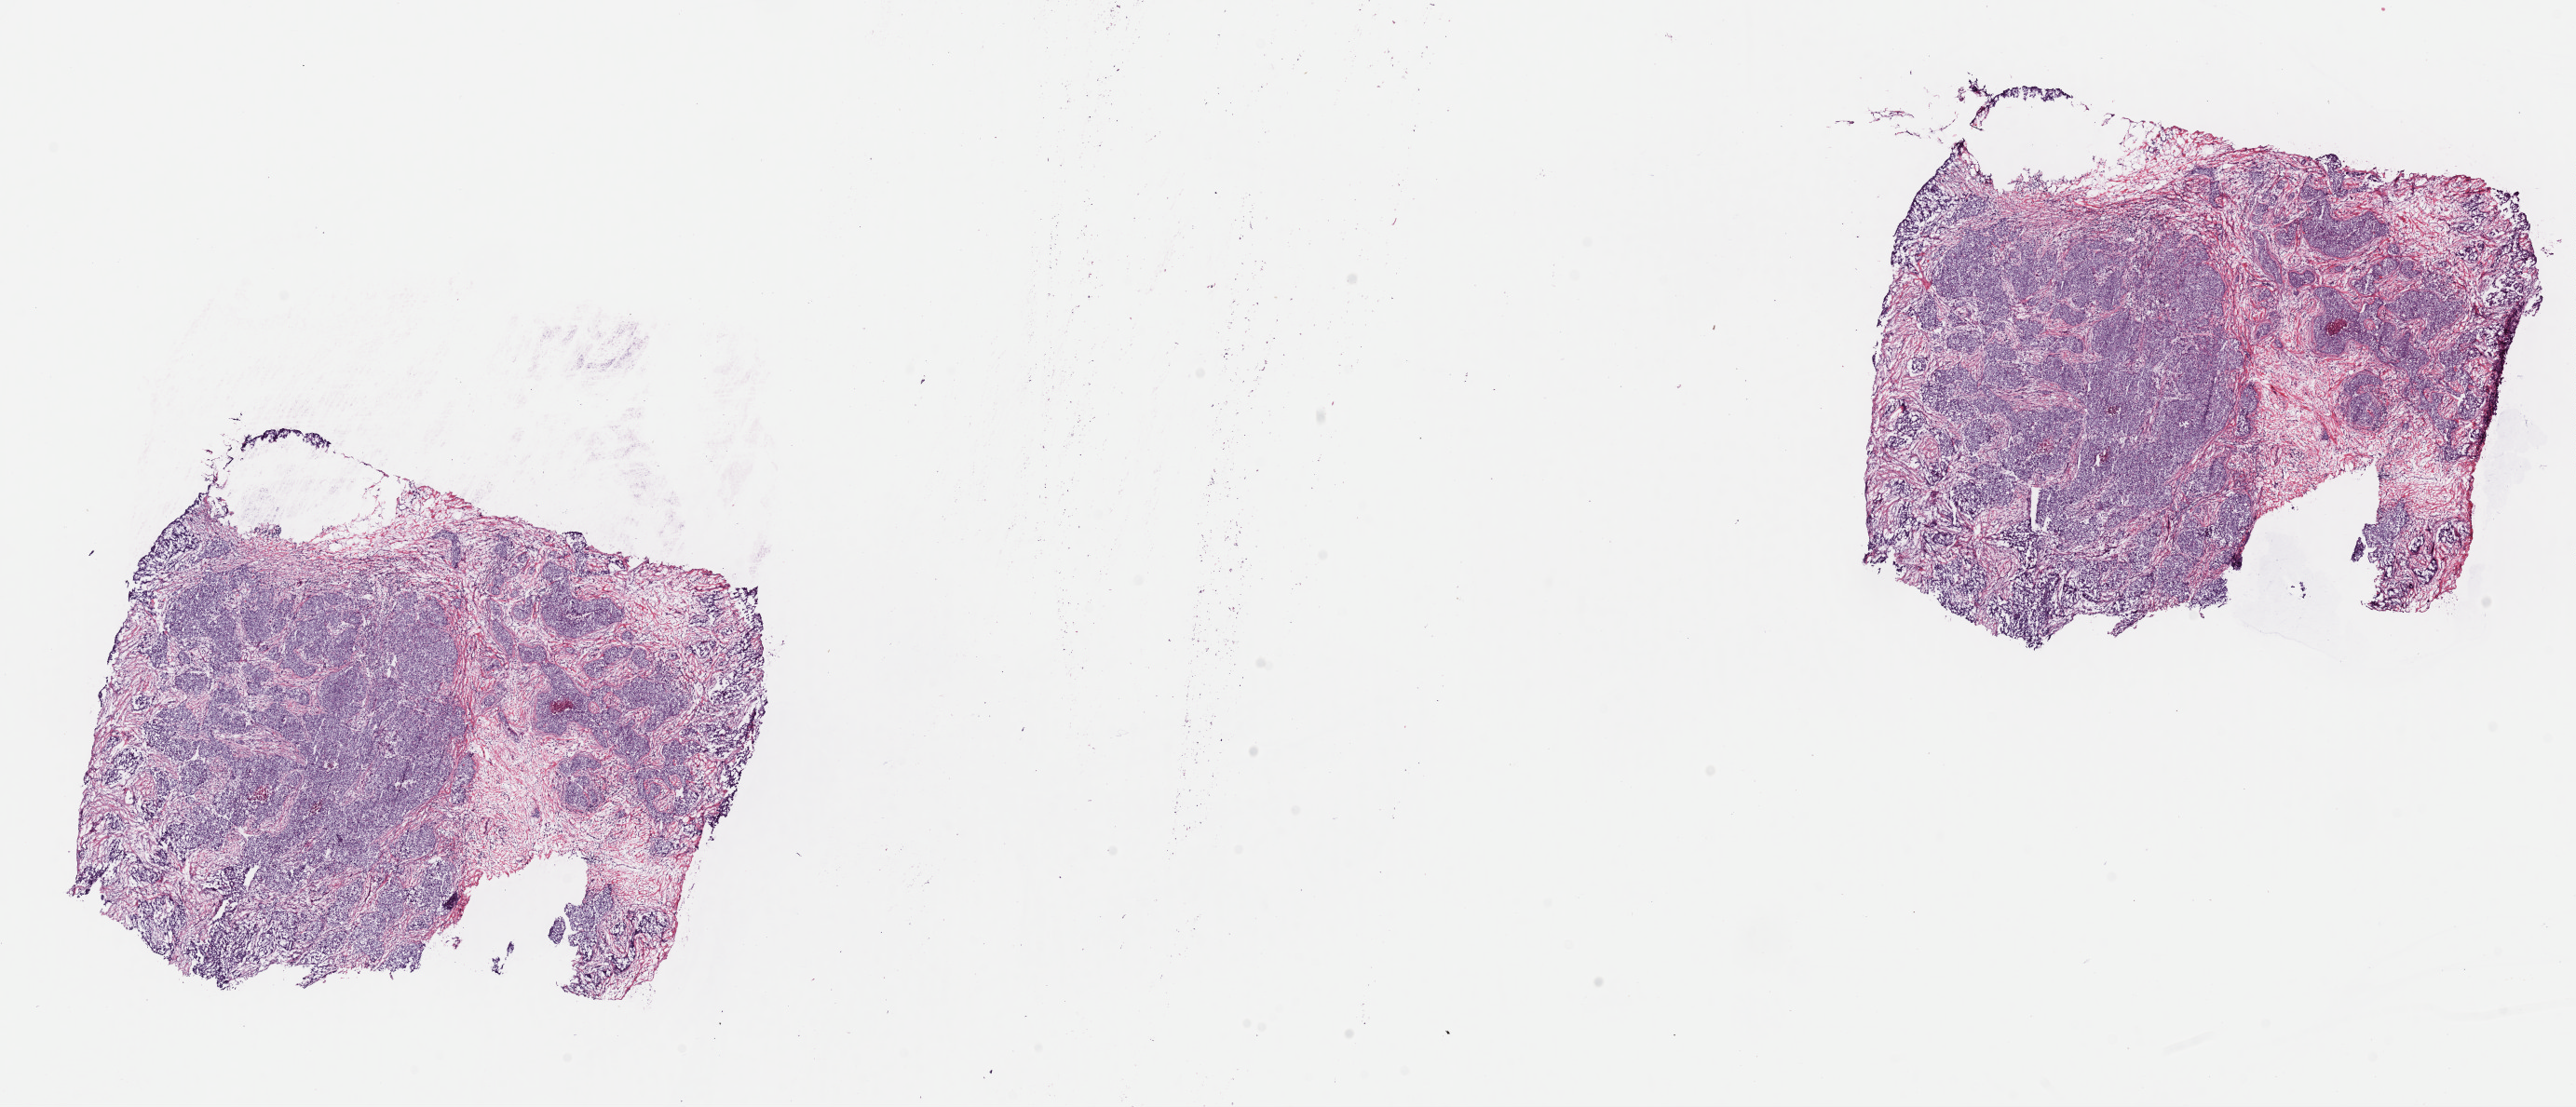
Hematoxylin and eosin (H&E) stained whole-slide image — a low-resolution overview of the entire scanned area, about 21.9 x 9.4 mm (from a 40x scan), frozen section from the top of the tissue portion, breast, primary tumour sample. Female patient; age at initial diagnosis 41 years. Slide review estimates, as recorded: tumour cells 80%, tumour nuclei 90%, normal cells 0%, stromal cells 15%, necrosis 5%. Inflammatory infiltration, as recorded: lymphocyte infiltration 0%, monocyte infiltration 0%, neutrophil infiltration 0%.
AJCC pathologic stage: IIB (6th edition). Laterality: left. Diagnosis: Infiltrating duct carcinoma, NOS. Lymph nodes positive (case pathology): 1 of 13 examined.